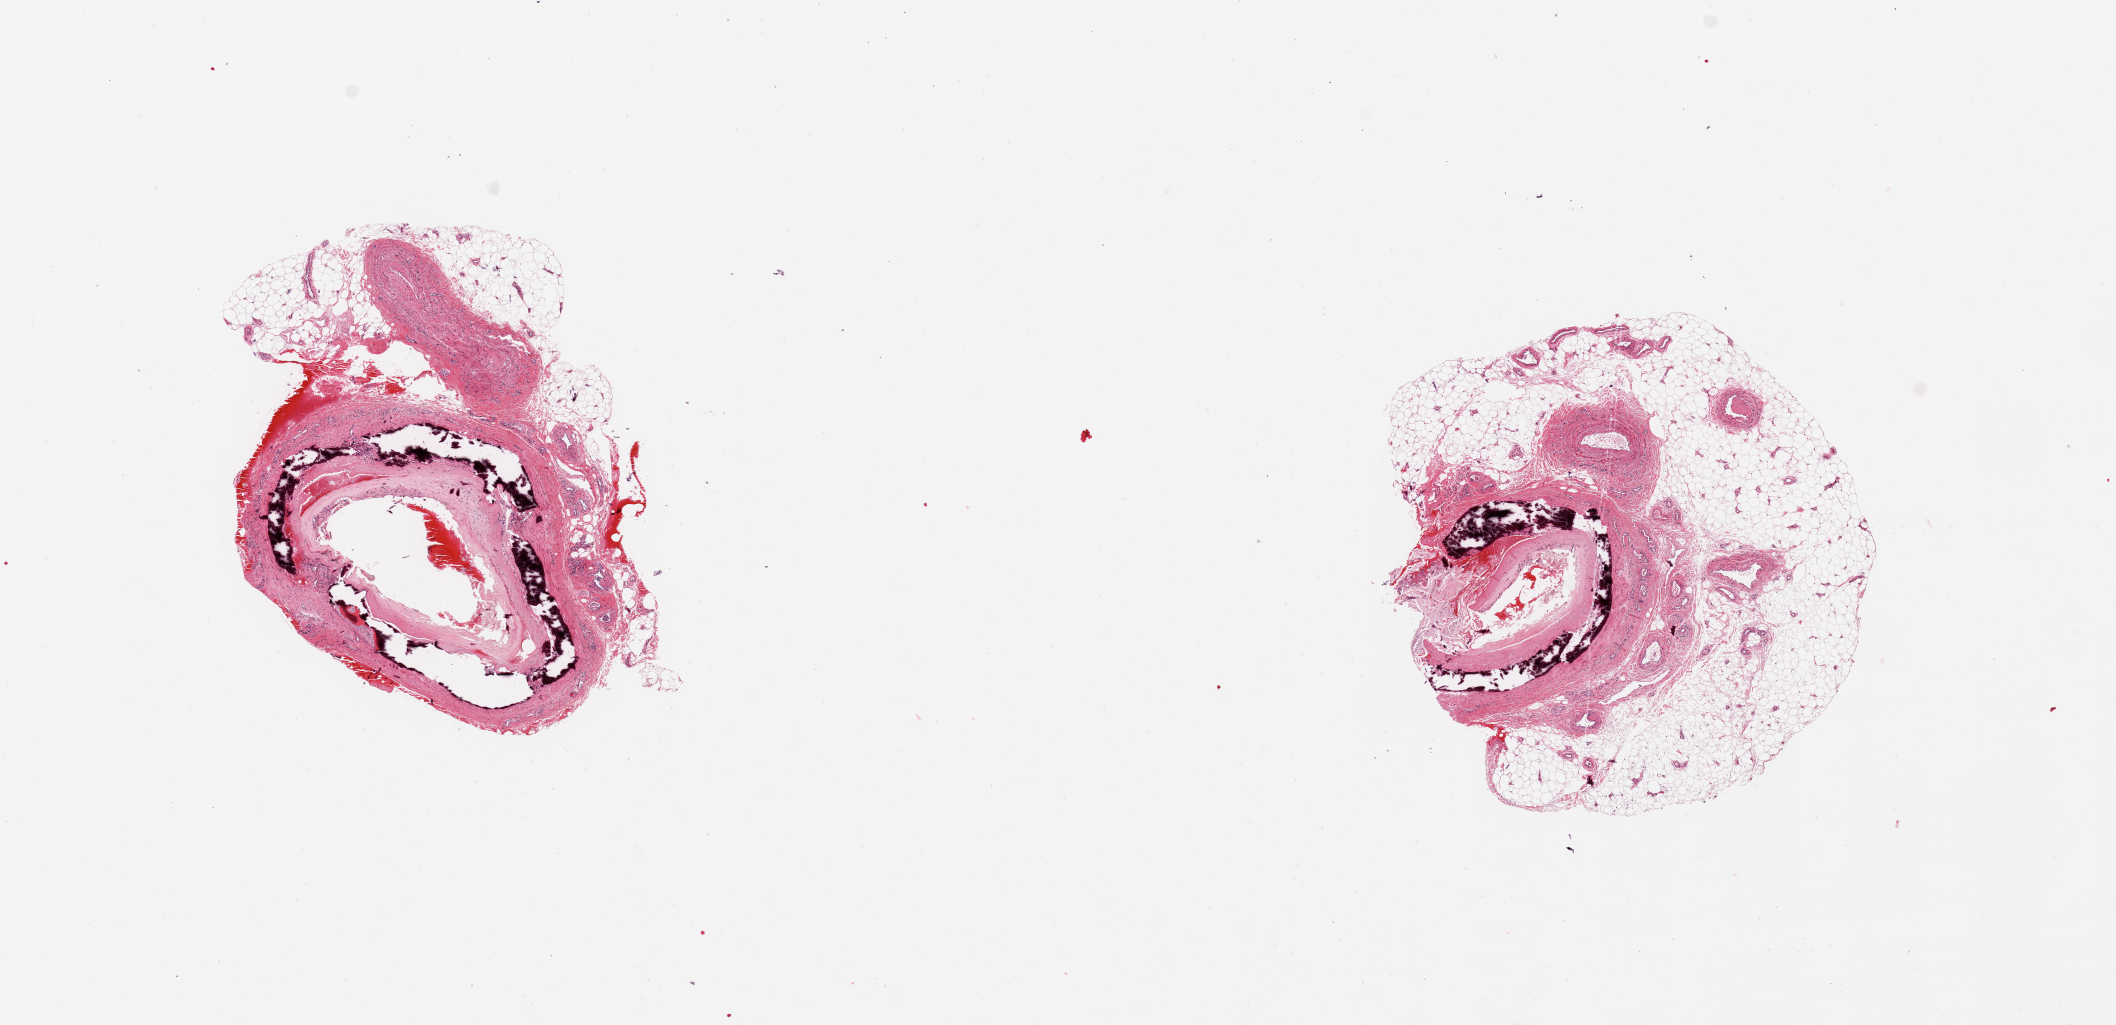
Hematoxylin and eosin (H&E) whole-slide image — shown as a low-resolution overview of the whole scanned area (about 16.7 x 8.1 mm, from a 20x scan); PAXgene-fixed, paraffin-embedded tissue; section of tibial artery (target tissue); tissue donor sample.
- reviewer comment on this tissue sample: 2 pieces adhrent fat/fibrous tissue up to ~2mm, marked calcified atherosis